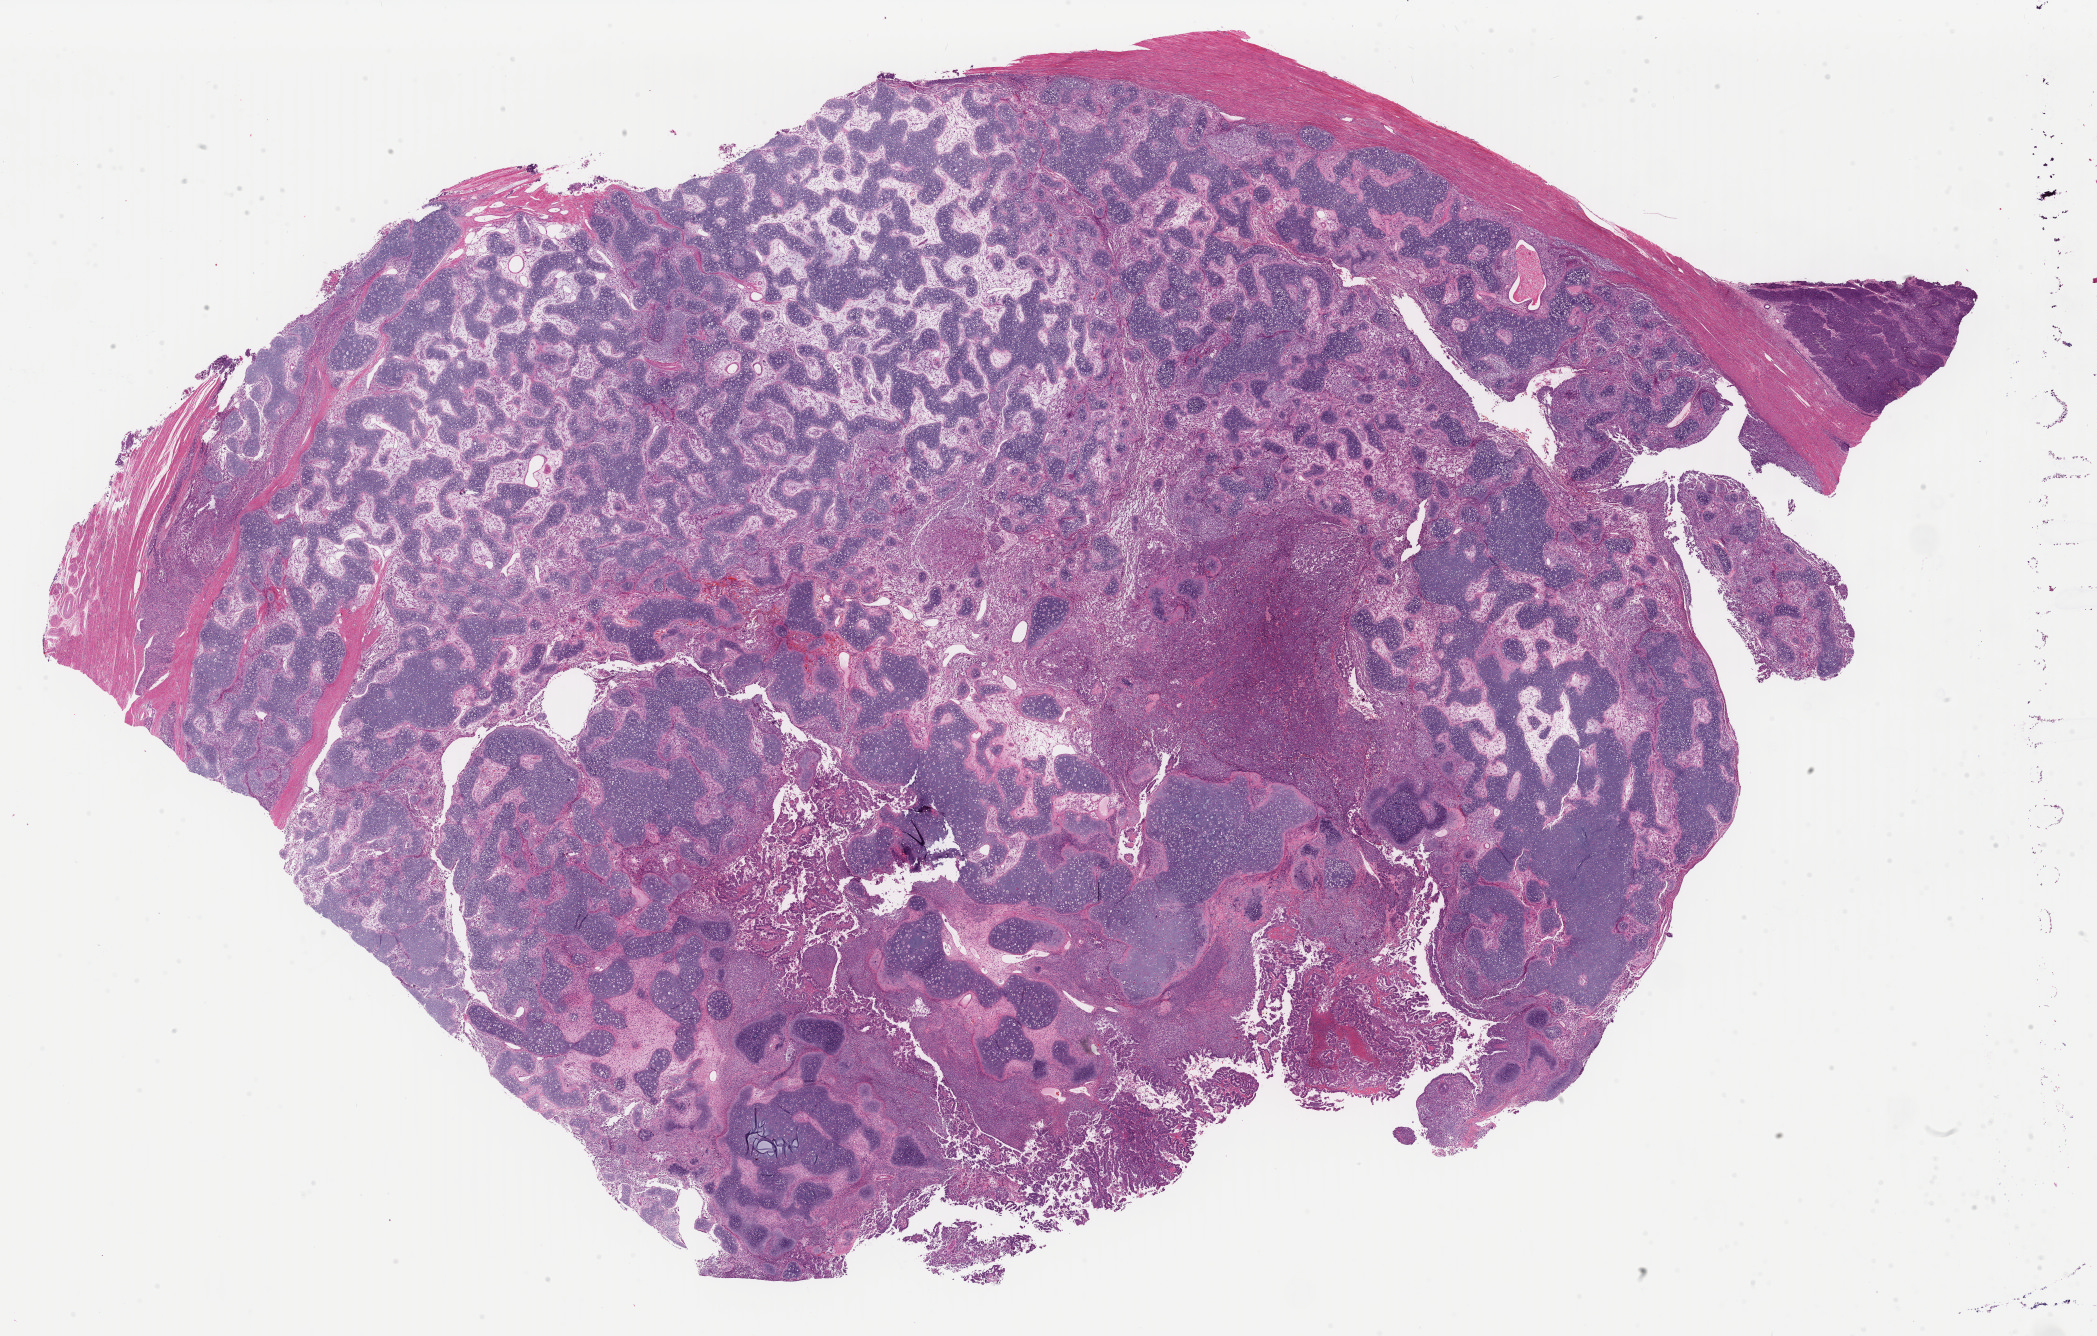
Hematoxylin and eosin (H&E) stained whole-slide image — a low-resolution overview of the entire scanned area, about 33.1 x 21.1 mm, FFPE section, primary tumour sample from the uterus. Patient sex: female.
• pathologic diagnosis: Mullerian mixed tumor
• FIGO stage: IC